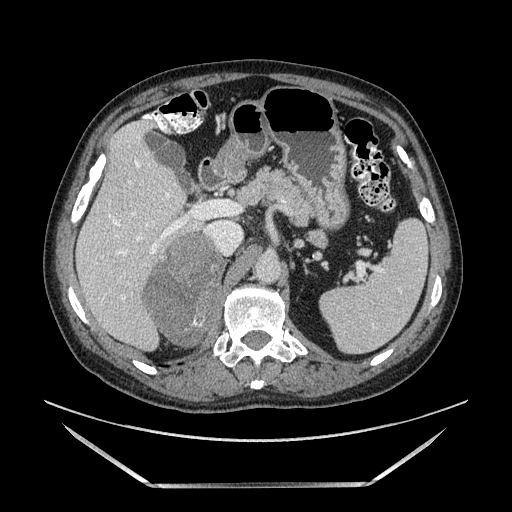
Contrast-enhanced abdominal CT, one axial slice. Slice 91 of 185 in the series (ordered by position). Soft-tissue window (W 400 / L 40 HU). 1.25 mm slice thickness. 512 × 512 image matrix. Male patient. Case-level facts recorded for this patient, not image findings: diagnosis: adrenocortical carcinoma; tumour side: right adrenal; tumour size at pathology: 10.3 cm; Ki-67 index: 20 %; stage (as recorded): 3.
Annotated regions visible in this slice (semi-automatically segmented with operator editing):
- mass: bounding box [x1, y1, x2, y2] px = [148, 234, 224, 345]